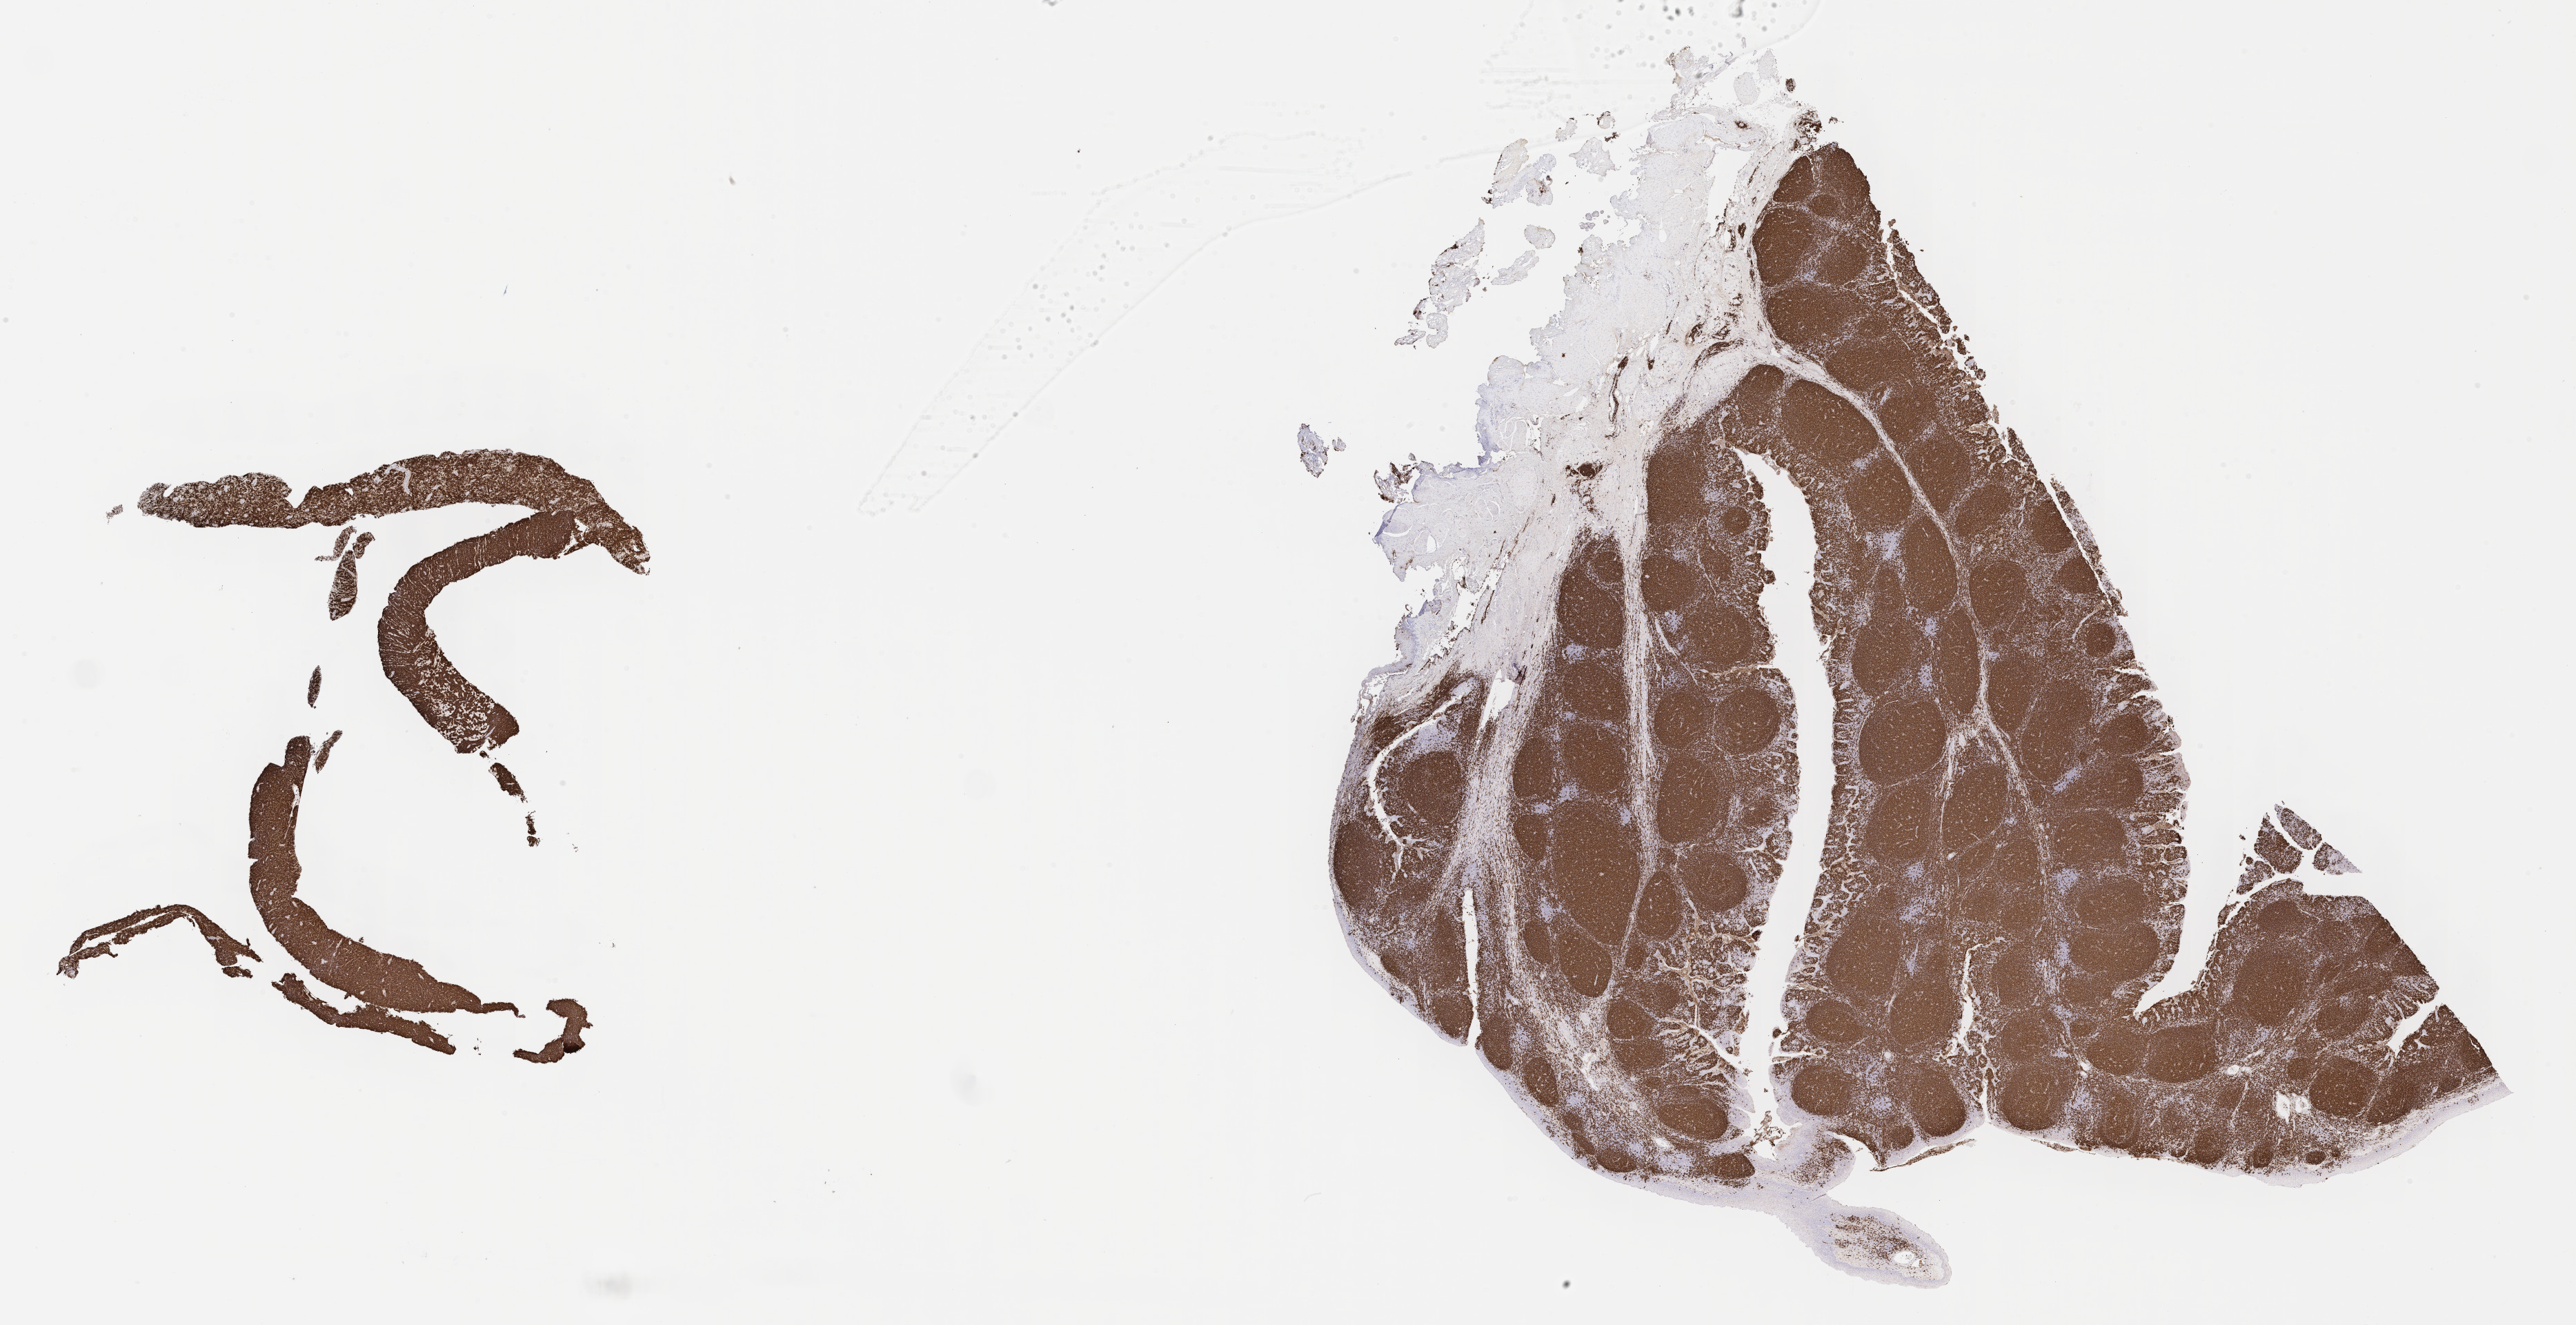
Immunohistochemistry (IHC) whole-slide image stained for CD20 — shown as a low-resolution overview of the whole scanned area (about 30.2 x 15.5 mm), tumor tissue, site: pleura. Male, age 2 years at initial diagnosis.
Diagnosis: Diffuse large B-cell lymphoma, NOS.